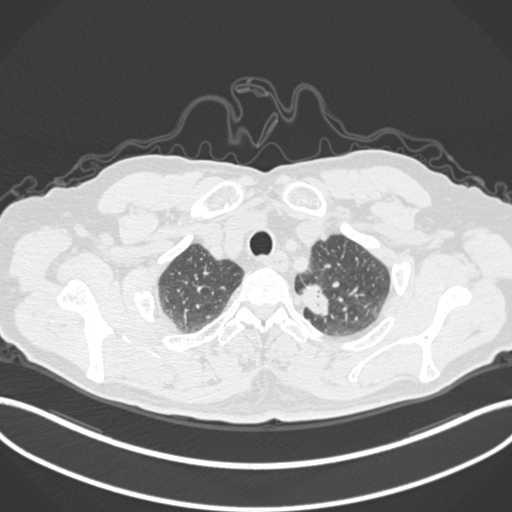
Chest CT, one axial slice; reconstruction kernel B30f; lung window (W 1500 / L -600 HU); 1 mm slice thickness; 512 × 512 image matrix, field of view 400 × 400 mm. Patient: male, 64 years. Case-level facts recorded for this patient, not image findings: clinical TNM (as recorded): T1c N0 M0.
Annotated regions visible in this slice (rectangle marked by the reading radiologist):
- lung tumour (recorded histology: adenocarcinoma): bounding box (x1, y1, x2, y2) in pixels: (298, 280, 339, 321)